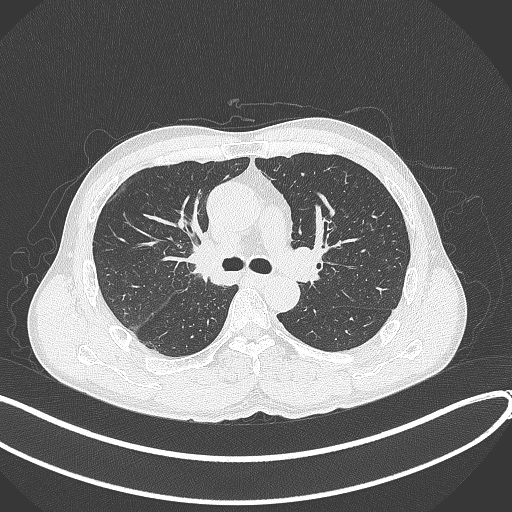
Chest CT, one axial slice. Position 243 of 409 along the scan axis. Reconstruction kernel B70f. Lung window (W 1500 / L -600 HU). 1 mm slice thickness. 512 × 512 image matrix, field of view 400 × 400 mm. Patient: male, 53 years. From the clinical record (not read from this slice): clinical TNM (as recorded): T1b N0 M0.
Annotated regions visible in this slice (rectangle marked by the reading radiologist):
- lung tumour (recorded histology: squamous cell carcinoma): bounding box (x1, y1, x2, y2) in pixels: (187, 237, 226, 291)